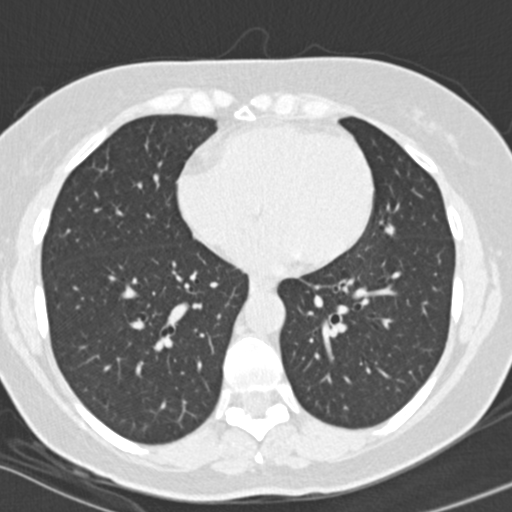
Axial slice from a low-dose chest CT screening exam. Baseline screening round. Lung window (W 1500 / L -600 HU). Standard (soft-tissue) reconstruction kernel (B30f). 120 kVp. 512 × 512 image matrix, field of view 288 × 288 mm. Female participant, aged 56 years at enrolment. Former smoker at enrolment.
- Lesion marked by an expert reader, bounding box [x1, y1, x2, y2] px = [366, 211, 409, 251].
- Reader record for this screening exam (exam-level; its link to the box is not recorded): non-calcified nodule or mass ≥4 mm, lingula, 7 × 5 mm, smooth margins, soft tissue attenuation.
- Official screen result: positive, change unspecified: nodule(s) >= 4 mm or enlarging nodule(s), mass(es), or other non-specific abnormalities suspicious for lung cancer.
- Later outcome: lung cancer diagnosed 863 days after this screen (after the third annual screen) — adenocarcinoma, NOS, left upper lobe, poorly differentiated (G3), stage IIIA (AJCC 6th edition), 15 mm at pathology.